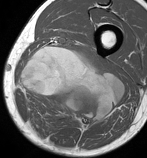
MRI of an extremity soft-tissue mass, one axial slice; position 43 of 86 along the scan axis; MR volume resampled by the dataset authors to the PET/CT grid (not the native acquisition matrix); 3.27 mm slice thickness; 147 × 158 image matrix. Male patient. Case-level facts recorded for this patient, not image findings: histological type: undifferentiated pleomorphic liposarcoma; grade: high; site of the primary tumour: left thigh.
Structures marked on this image (expert contour drawn on MRI and transferred to this co-registered scan by the dataset authors):
- gross tumour volume including surrounding oedema: bounding box [x1, y1, x2, y2] px = [19, 46, 125, 130]
- gross tumour volume (mass): [21, 46, 125, 130]